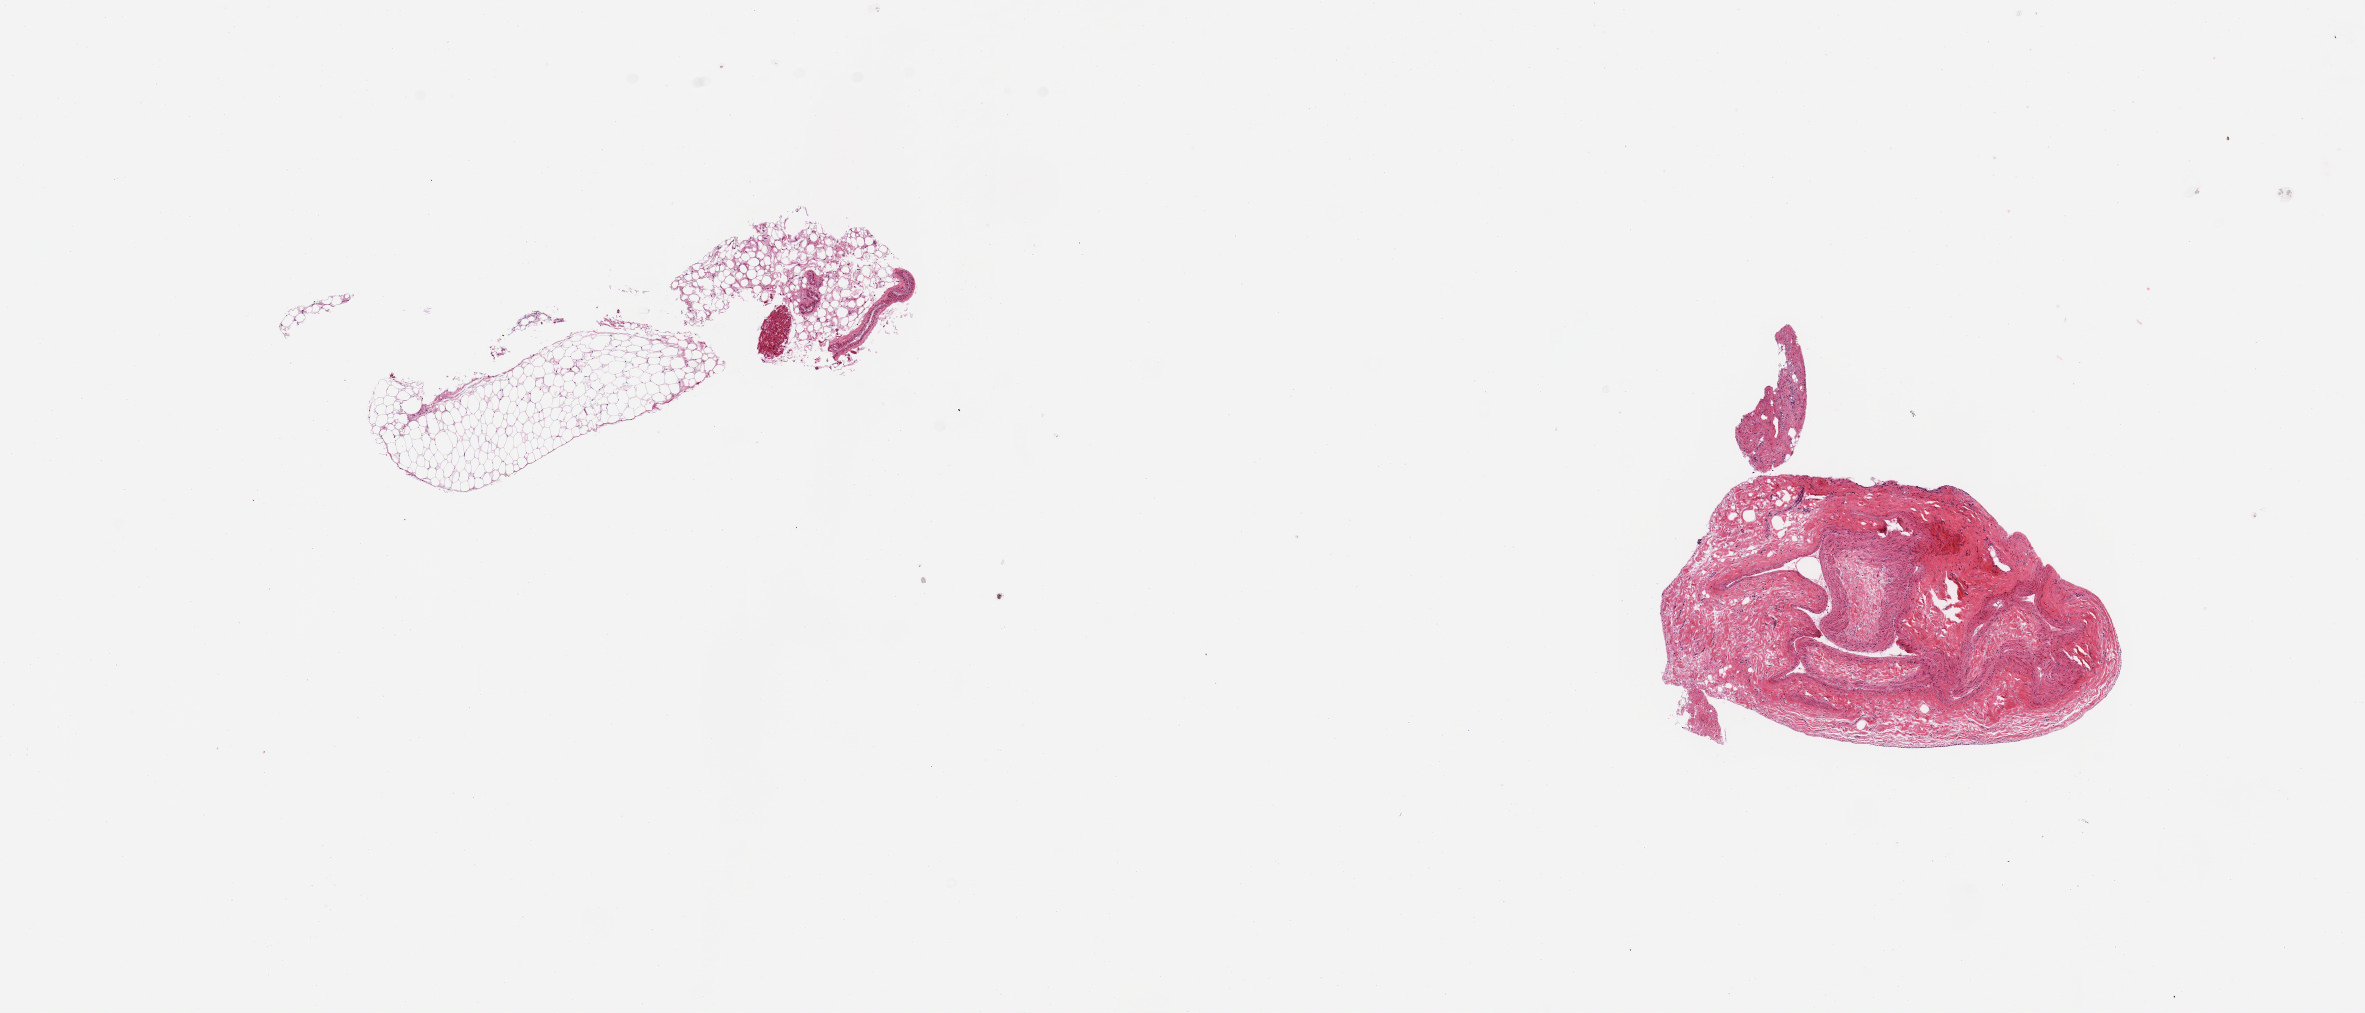
H&E whole-slide image — shown as a low-resolution overview of the whole scanned area (about 18.7 x 8.0 mm, from a 20x scan), PAXgene-fixed paraffin-embedded (PFPE) section, sampled site (target tissue): coronary artery, tissue donor sample. Donor: female.
Reviewer comment on this tissue sample: 2 pieces; fat and vein.